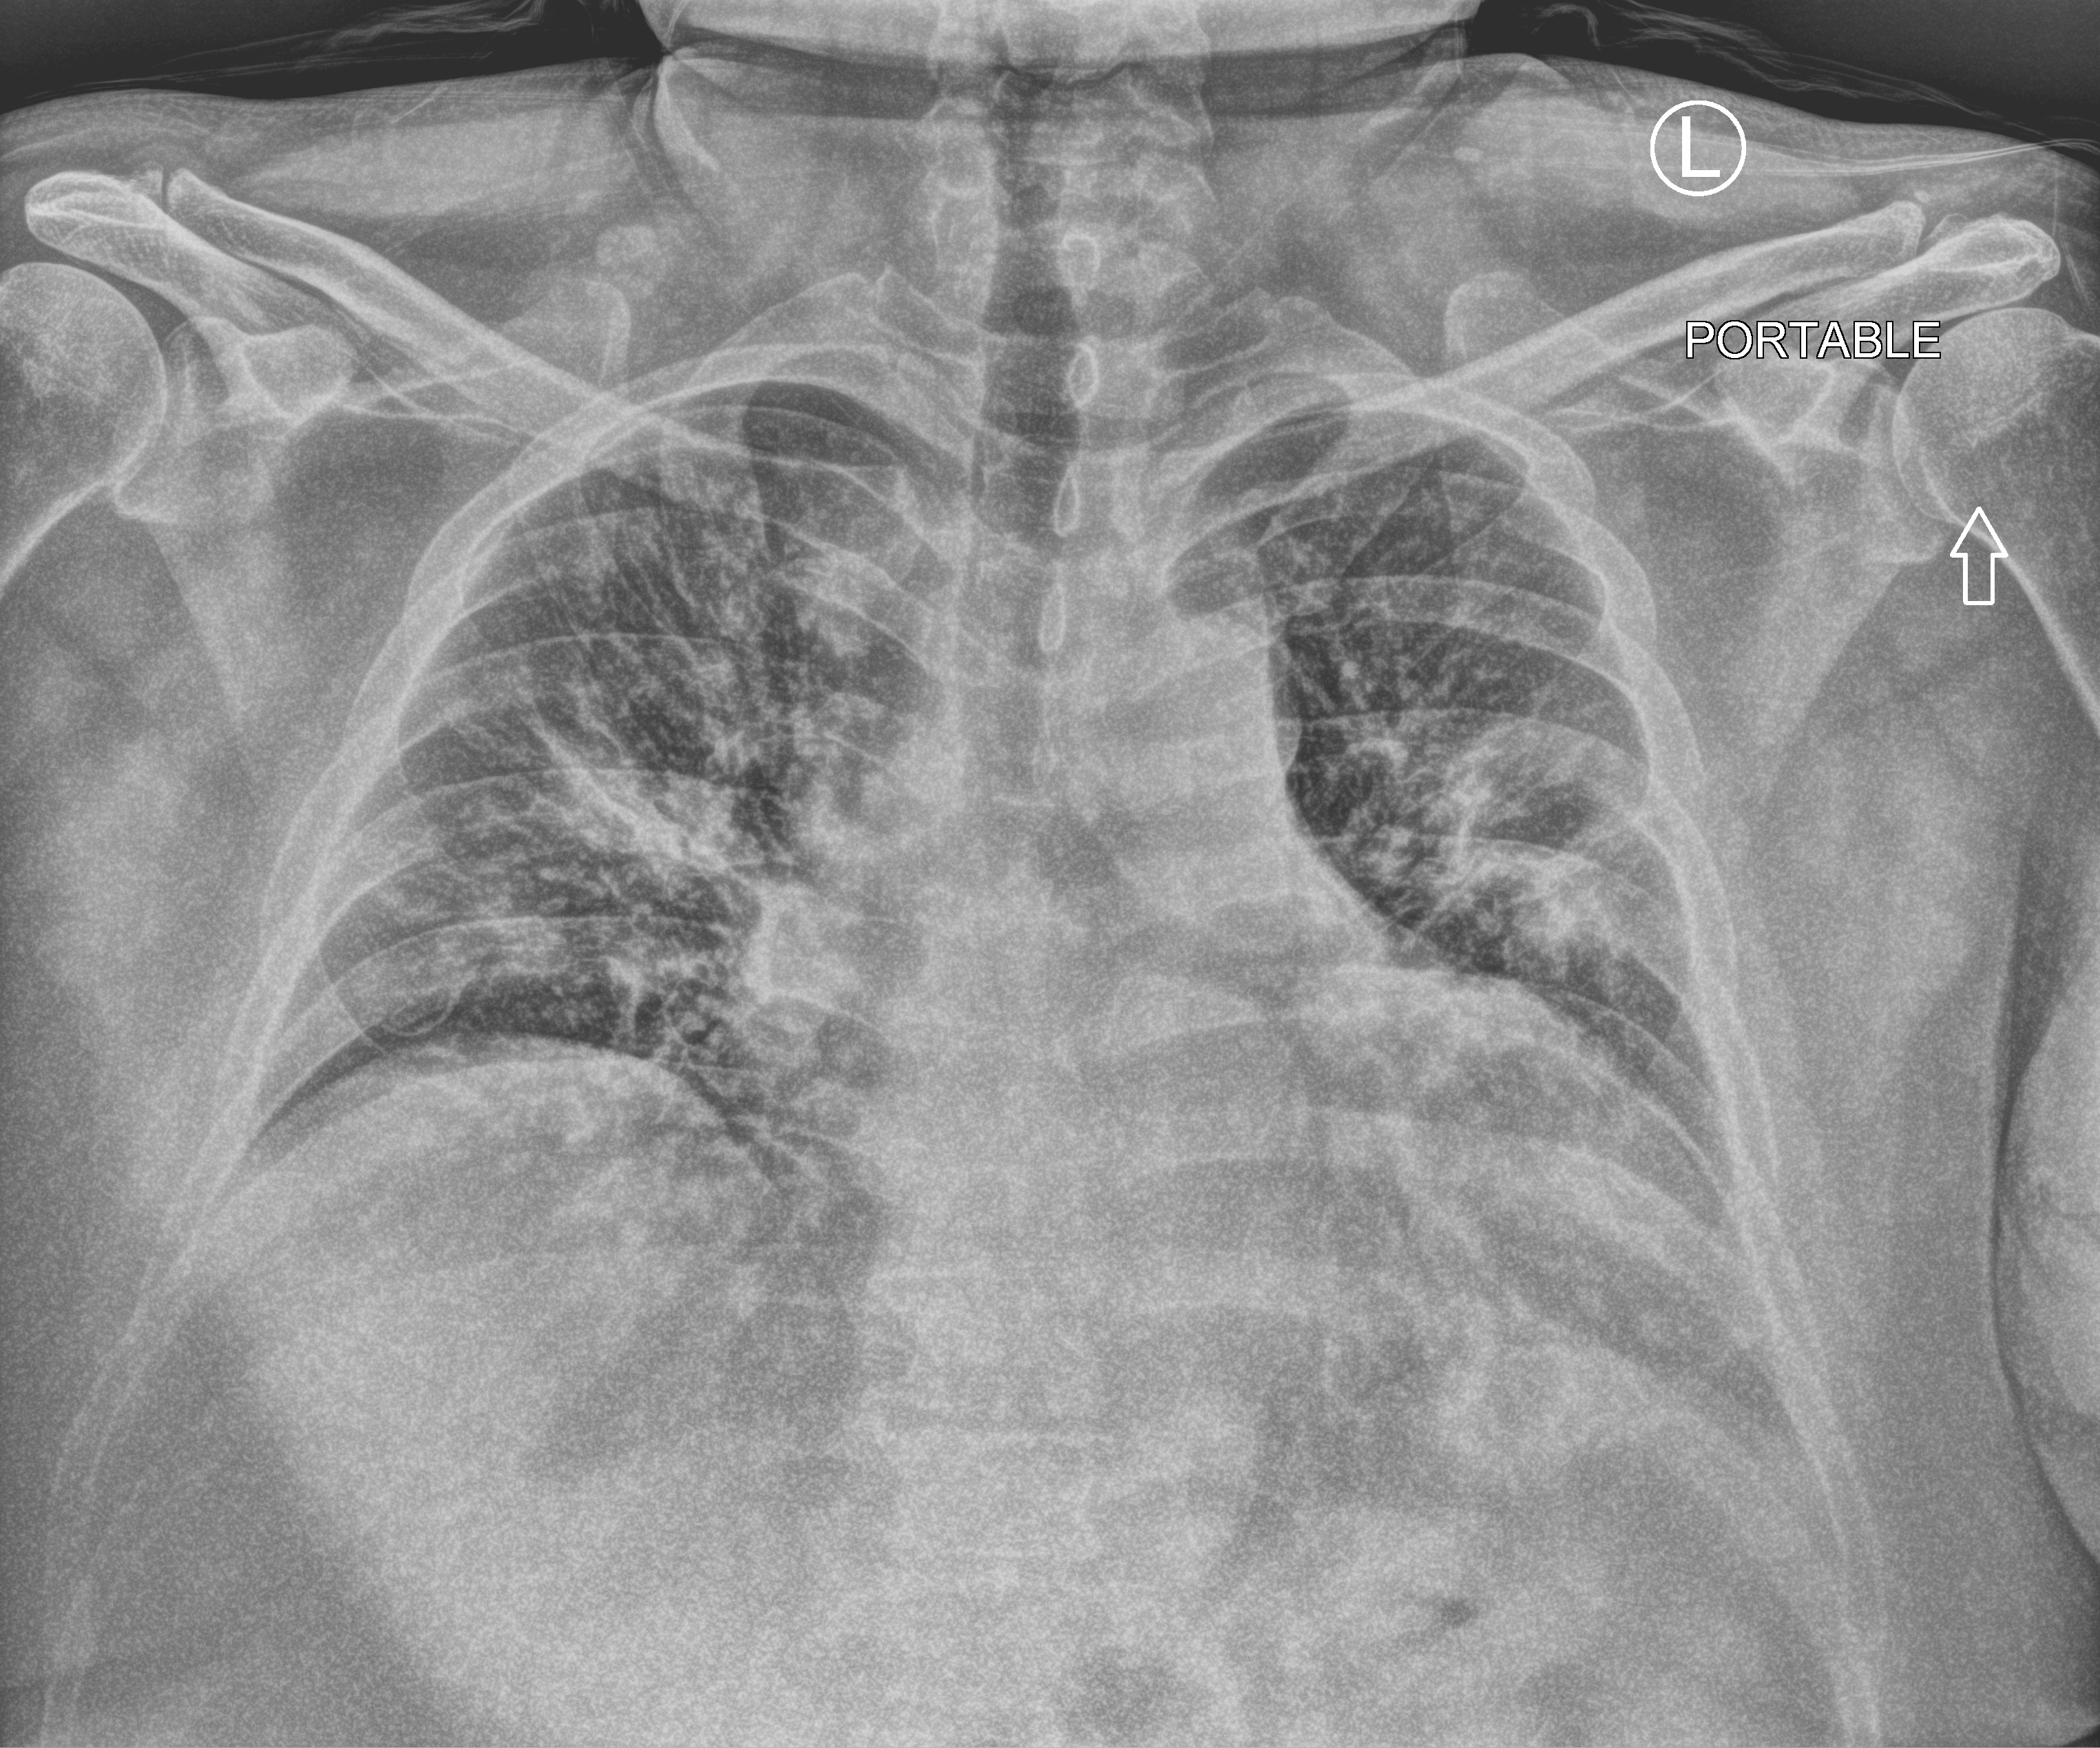
Bedside chest radiograph (computed radiography), anteroposterior (AP) projection. Patient hospitalised with COVID-19; male, aged 18–59 years.
Admission-level facts for this patient (not findings on this image; timing relative to this image not recorded):
- mechanically ventilated during this hospital stay: no